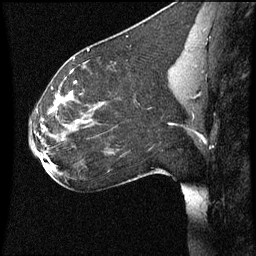
Breast MRI (dynamic contrast-enhanced), one sagittal slice. Position 33 of 60 along the scan axis. Dynamic contrast-enhanced series, image 2 of 3 at this slice position (ordered by acquisition). 1.5 T. TE 4.2 ms, TR 8.9 ms. 256 × 256 image matrix. Patient: female, 35 years. Case-level facts recorded for this patient, not image findings: setting: breast cancer imaged before/during neoadjuvant chemotherapy; receptor status: HER2-positive.
Outlined on this slice (semi-automatically segmented with operator editing):
- analysis volume of interest (the breast-tissue region the enhancement analysis was run in; not a lesion): bounding box (x1, y1, x2, y2) in pixels: (28, 66, 177, 177)
- tumour enhancement mask (voxels above the 70 % enhancement threshold inside the analysis volume of interest): (42, 90, 79, 157)